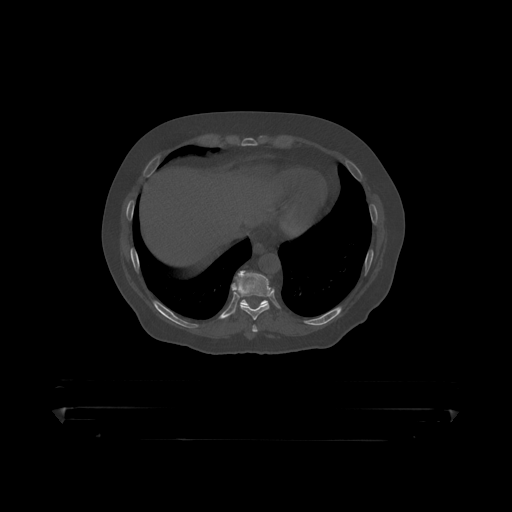
CT including the spine, one axial slice. Position 232 of 390 along the scan axis. 120 kVp. Bone window (W 1800 / L 400 HU). 1.25 mm slice thickness. 512 × 512 image matrix. Male patient, age 60 years. Case-level facts recorded for this patient, not image findings: primary cancer: prostate.
Structures marked on this image (semi-automatically segmented with operator editing):
- T10 vertebra: bounding box [x1, y1, x2, y2] px = [240, 300, 268, 306]
- T9 vertebra: [232, 271, 271, 319]